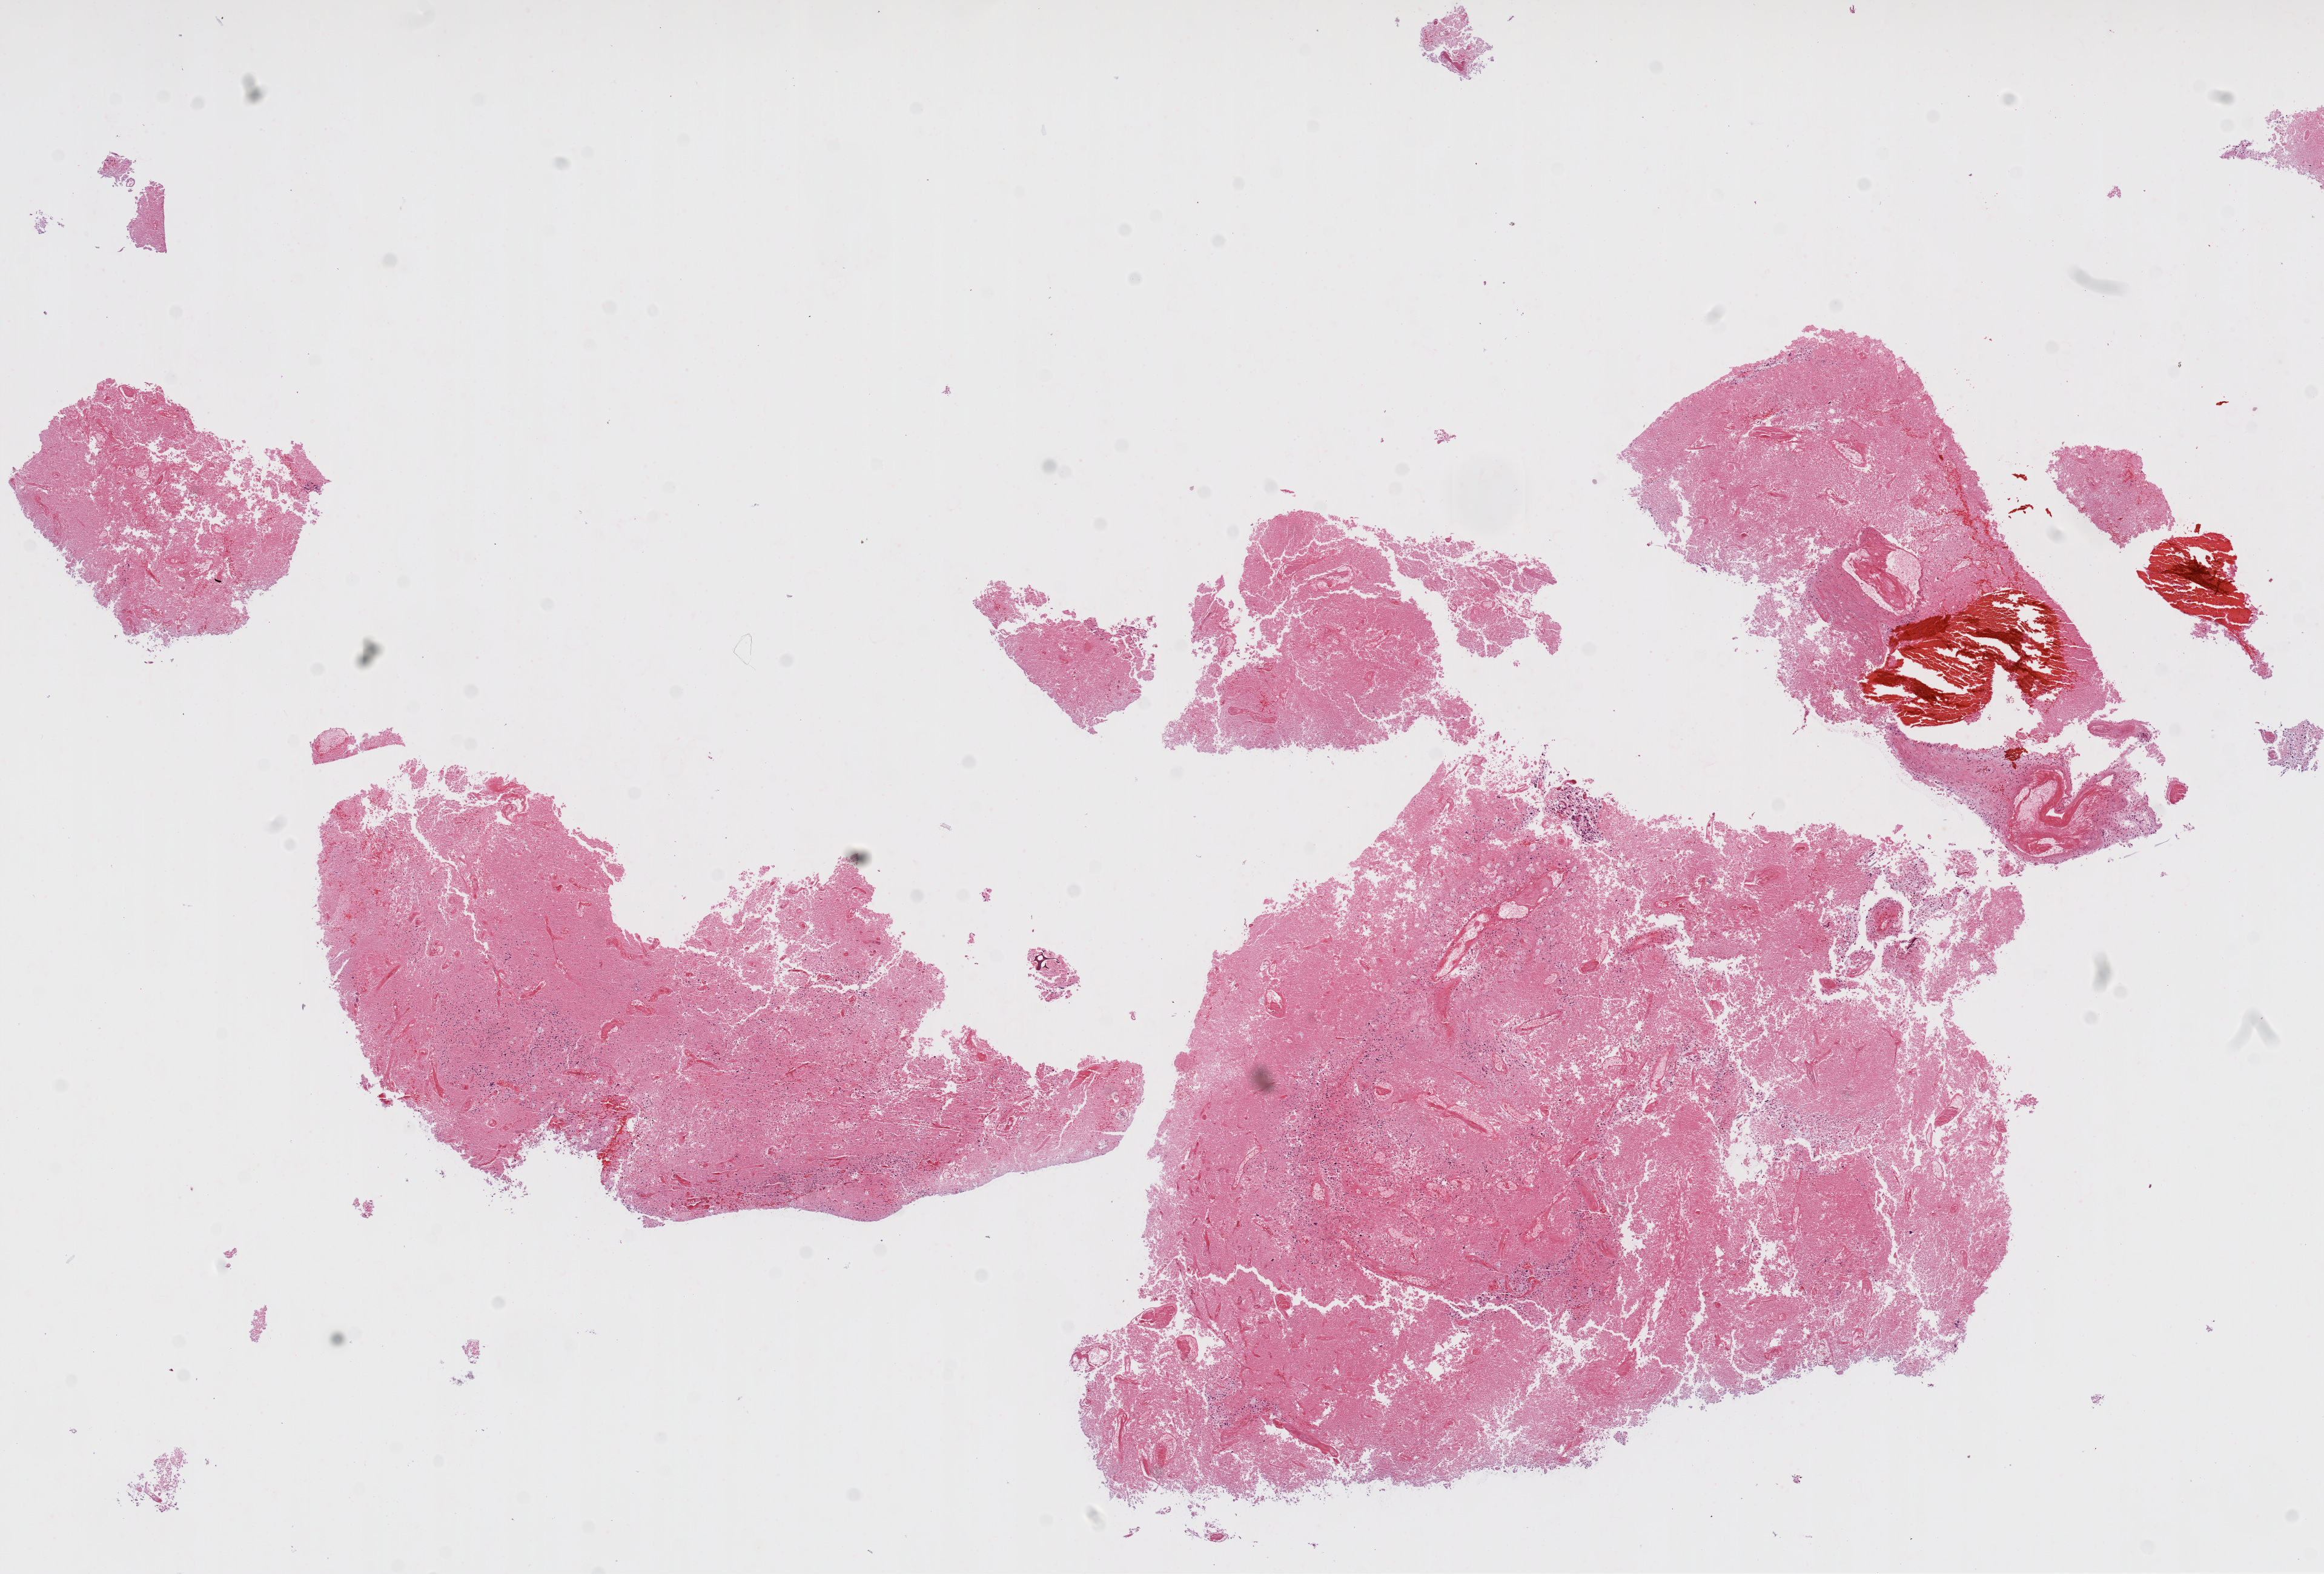
Digitized H&E tissue section (whole slide) — whole scanned area (about 15.5 x 10.5 mm, acquisition: 20x scan) shown as a low-resolution overview, formalin-fixed paraffin-embedded (FFPE) diagnostic section, brain, primary tumour sample. Female, age 55 years at initial diagnosis.
Diagnosis: Glioblastoma.